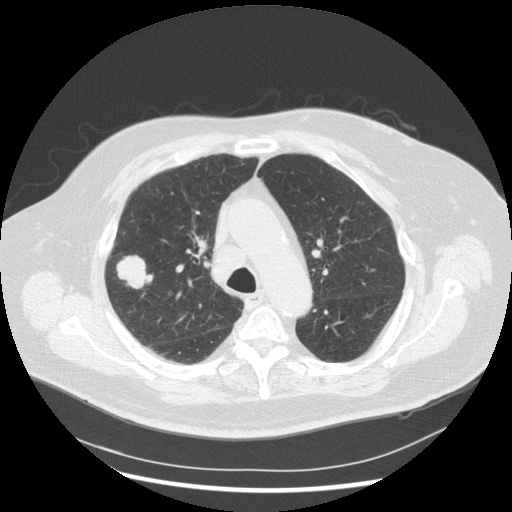
Low-dose screening chest CT, one axial slice; slice 196 of 263 in the series (ordered by position); 120 kVp; lung window (W 1500 / L -600 HU); 2.5 mm slice thickness; 512 × 512 image matrix, field of view 400 × 400 mm.
Structures marked on this image (outlined manually by an expert reader):
- lesion 1 (tumor, upper lobe of right lung): bounding box (x1, y1, x2, y2) in pixels: (117, 256, 153, 288)